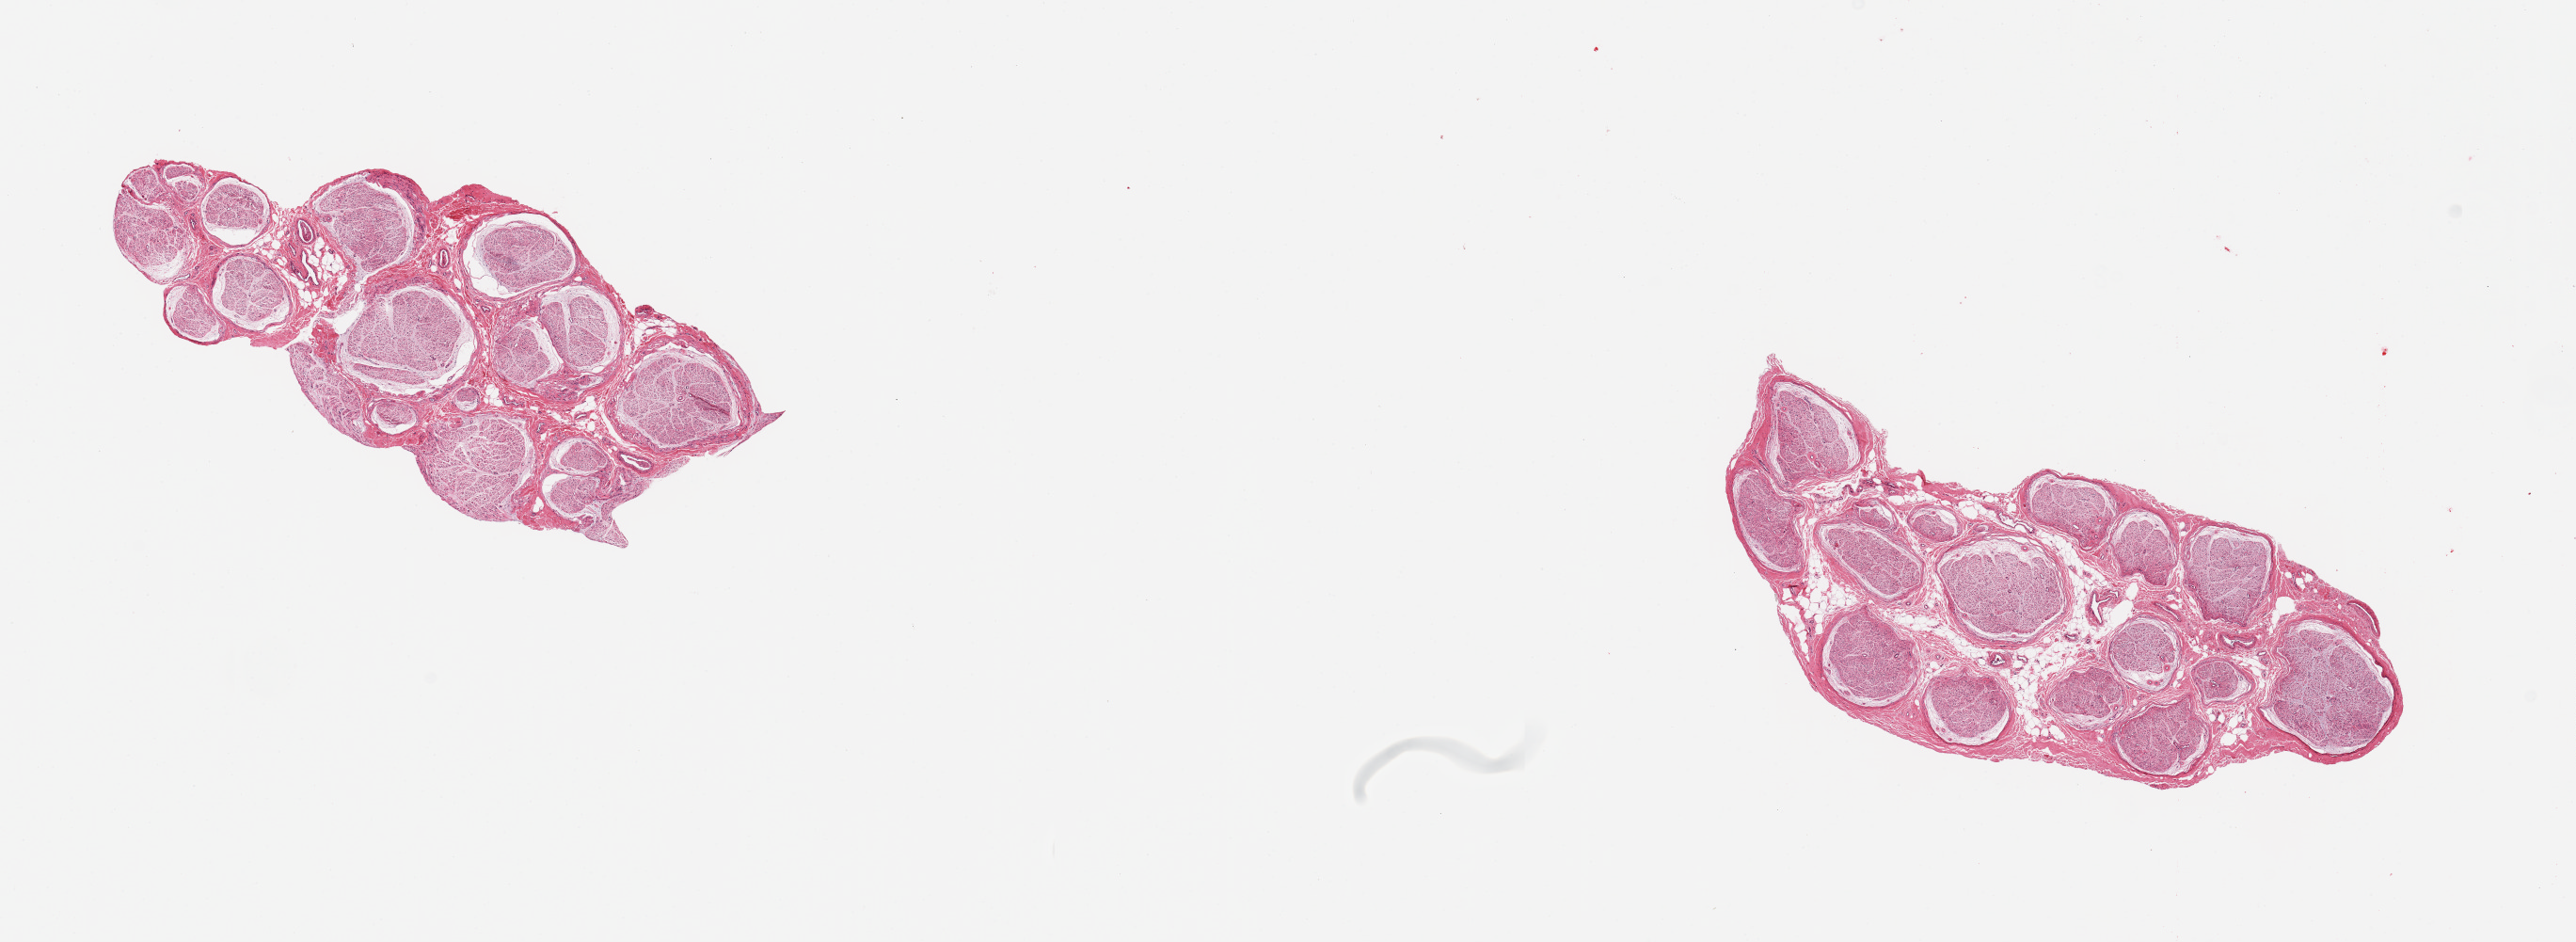
H&E whole-slide image, brightfield, low-resolution overview of the scanned area, about 21.7 x 7.9 mm (slide scanned at 20x). PAXgene-fixed, paraffin-embedded tissue. Target tissue: tibial nerve. Tissue donor sample. Donor sex: male.
Reviewer comment on this tissue sample: 2 pieces, clean specimens, no adherent fat.